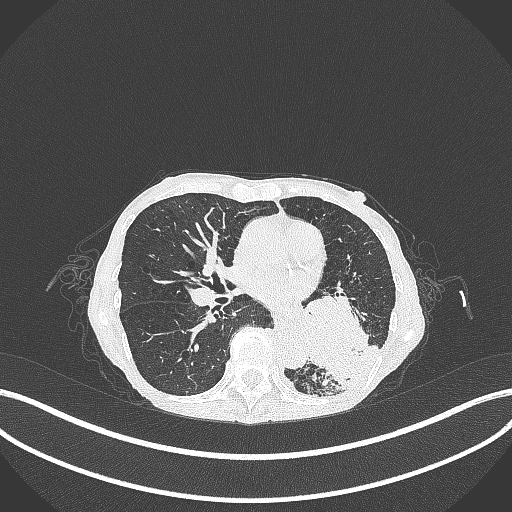
Chest CT, one axial slice. Slice 131 of 347 in the series (ordered by position). 120 kVp. Lung window (W 1500 / L -600 HU). 1 mm slice thickness. 512 × 512 image matrix, field of view 400 × 400 mm. Patient: female, 70 years. From the clinical record (not read from this slice): clinical TNM (as recorded): T3 N0 M0; histopathological grade: G3.
Annotated regions visible in this slice (bounding box drawn by a radiologist):
- lung tumour (recorded histology: small cell carcinoma): bounding box (x1, y1, x2, y2) in pixels: (298, 283, 373, 396)